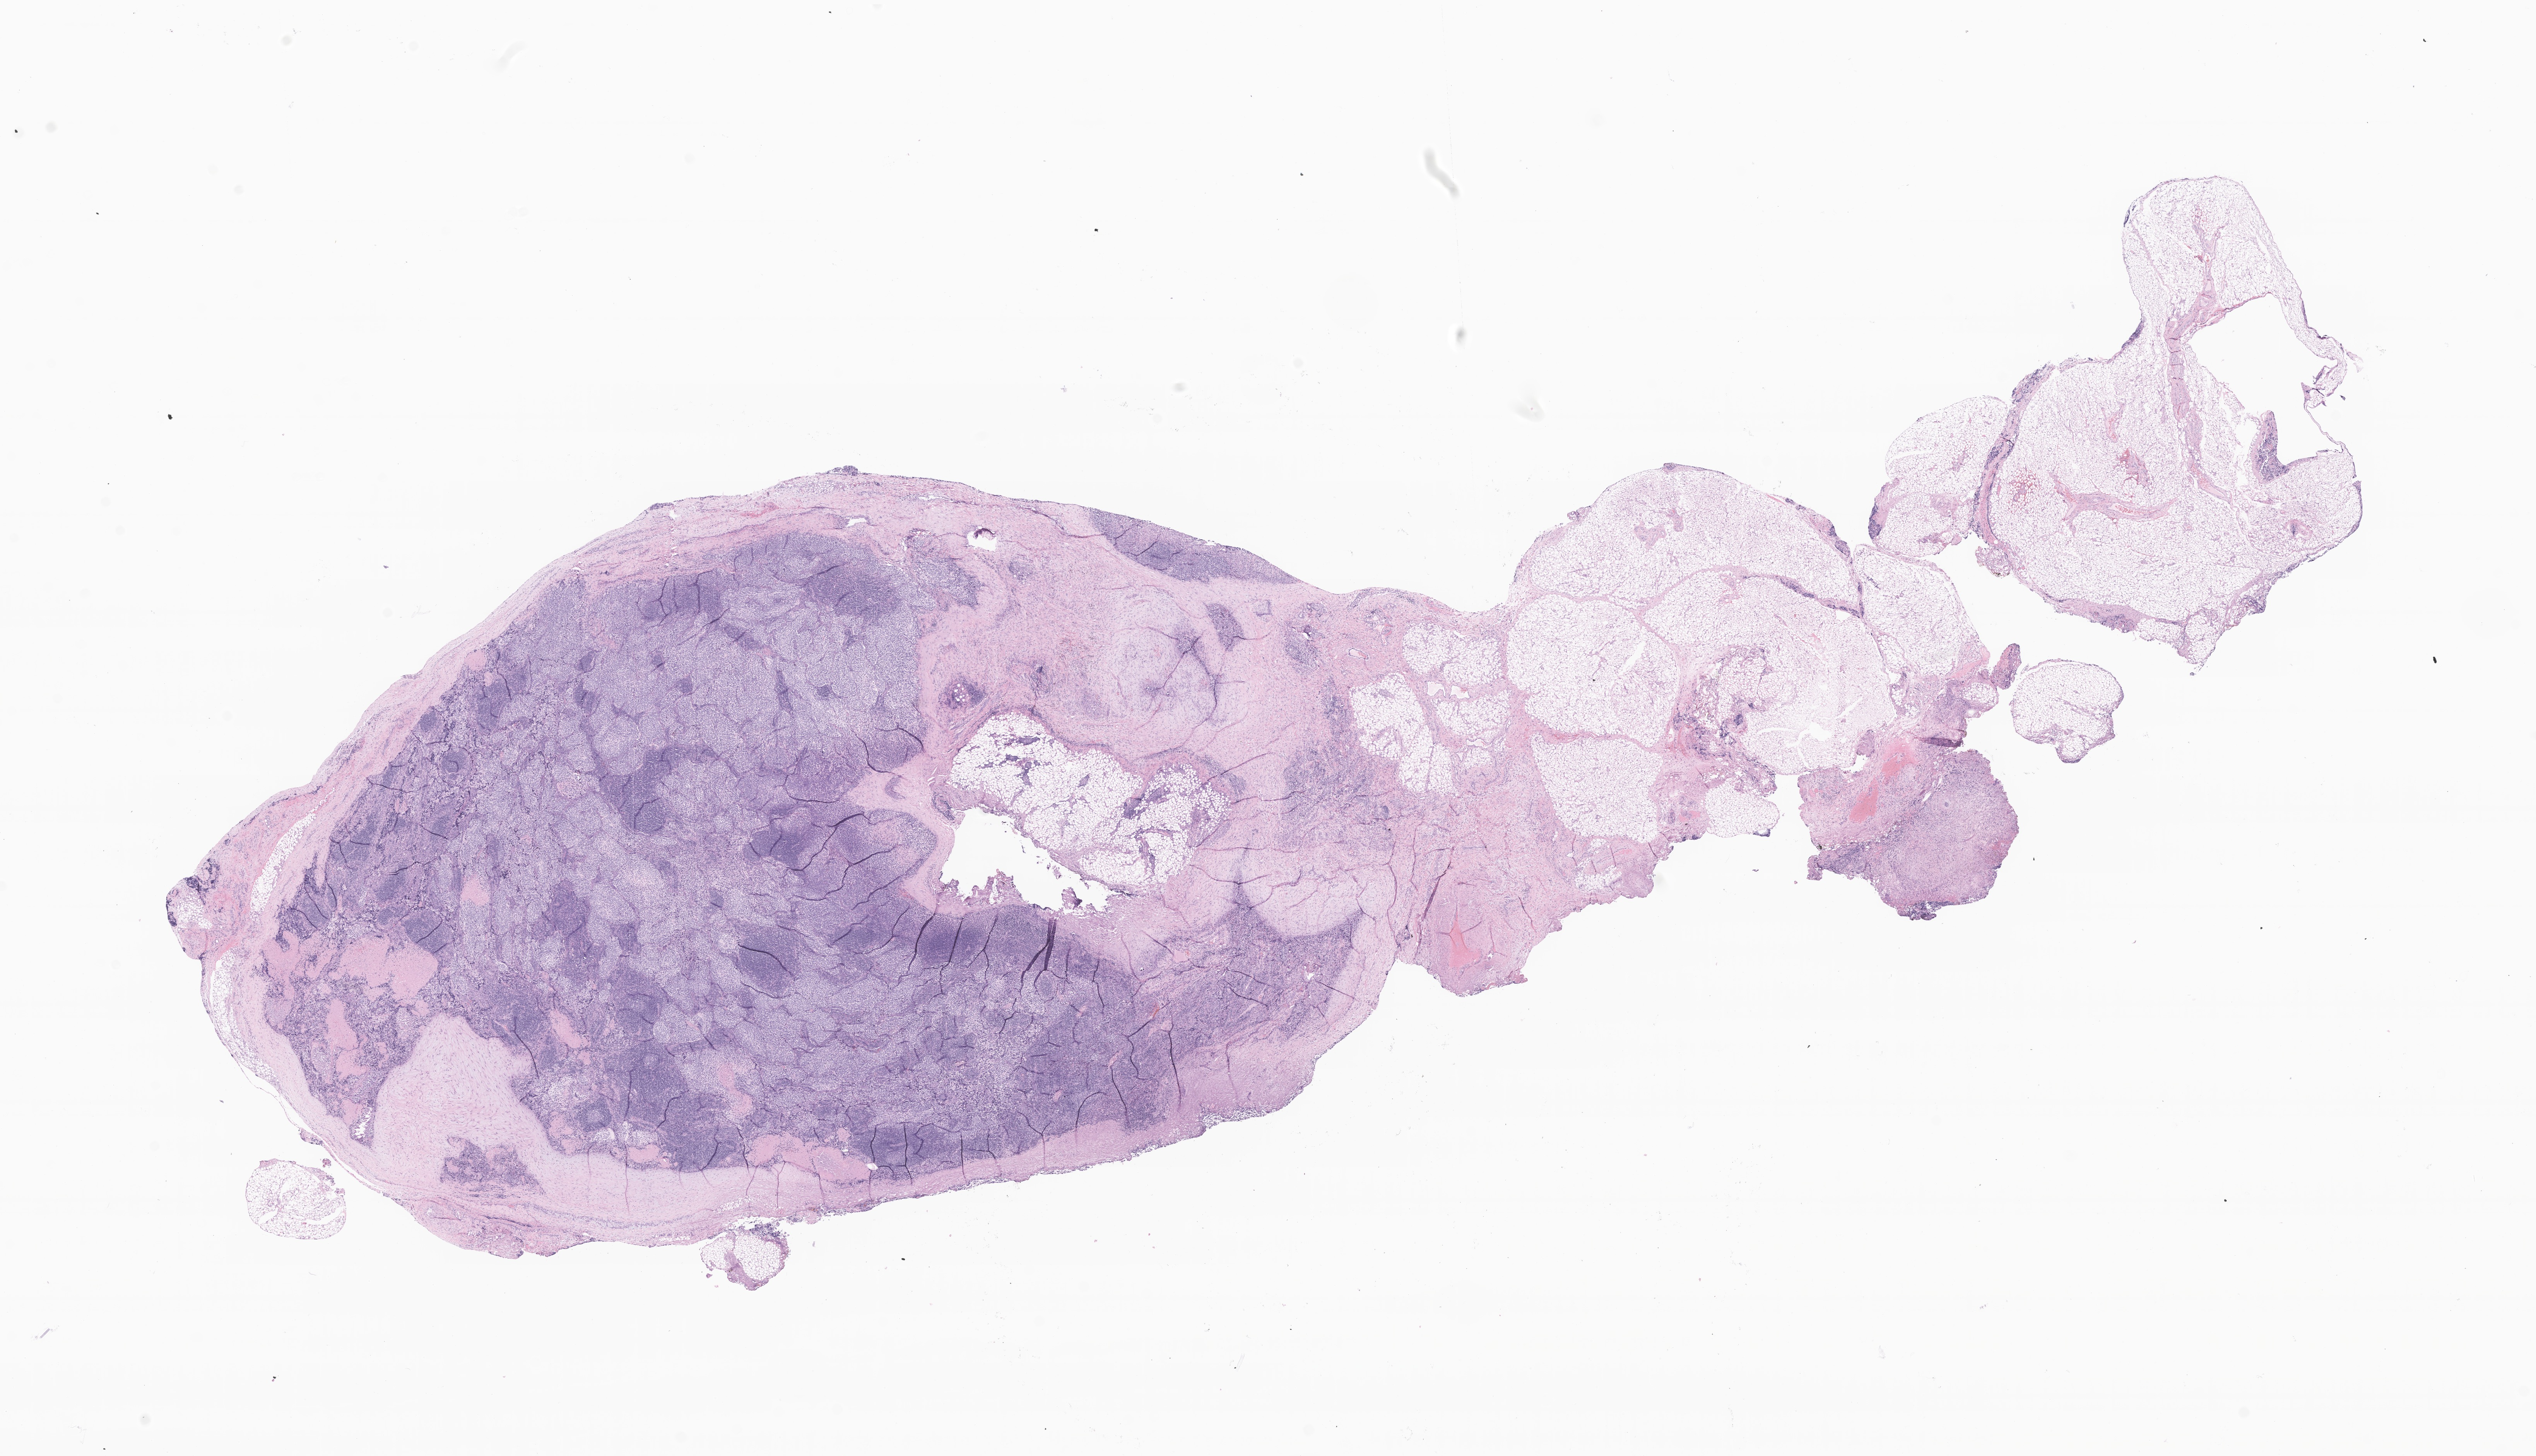
Whole-slide image, haematoxylin and eosin stain of tumor tissue from the retroperitoneum — shown as a low-resolution overview of the whole scanned area (about 27.6 x 15.9 mm); FFPE section. Female patient, age 911 days.
Diagnosis (ICD-O-3 morphology term): Neuroblastoma, NOS.